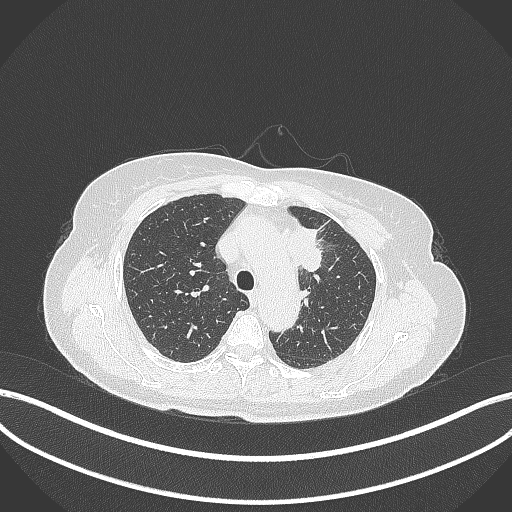
Chest CT, one axial slice; position 246 of 369 along the scan axis; reconstruction kernel B70f; 120 kVp; lung window (W 1500 / L -600 HU); 512 × 512 image matrix. Female patient, age 65 years. Case-level facts recorded for this patient, not image findings: clinical TNM (as recorded): T2a N0 M0.
Annotated regions visible in this slice (bounding box drawn by a radiologist):
- lung tumour (recorded histology: adenocarcinoma): bounding box (x1, y1, x2, y2) in pixels: (284, 225, 326, 274)